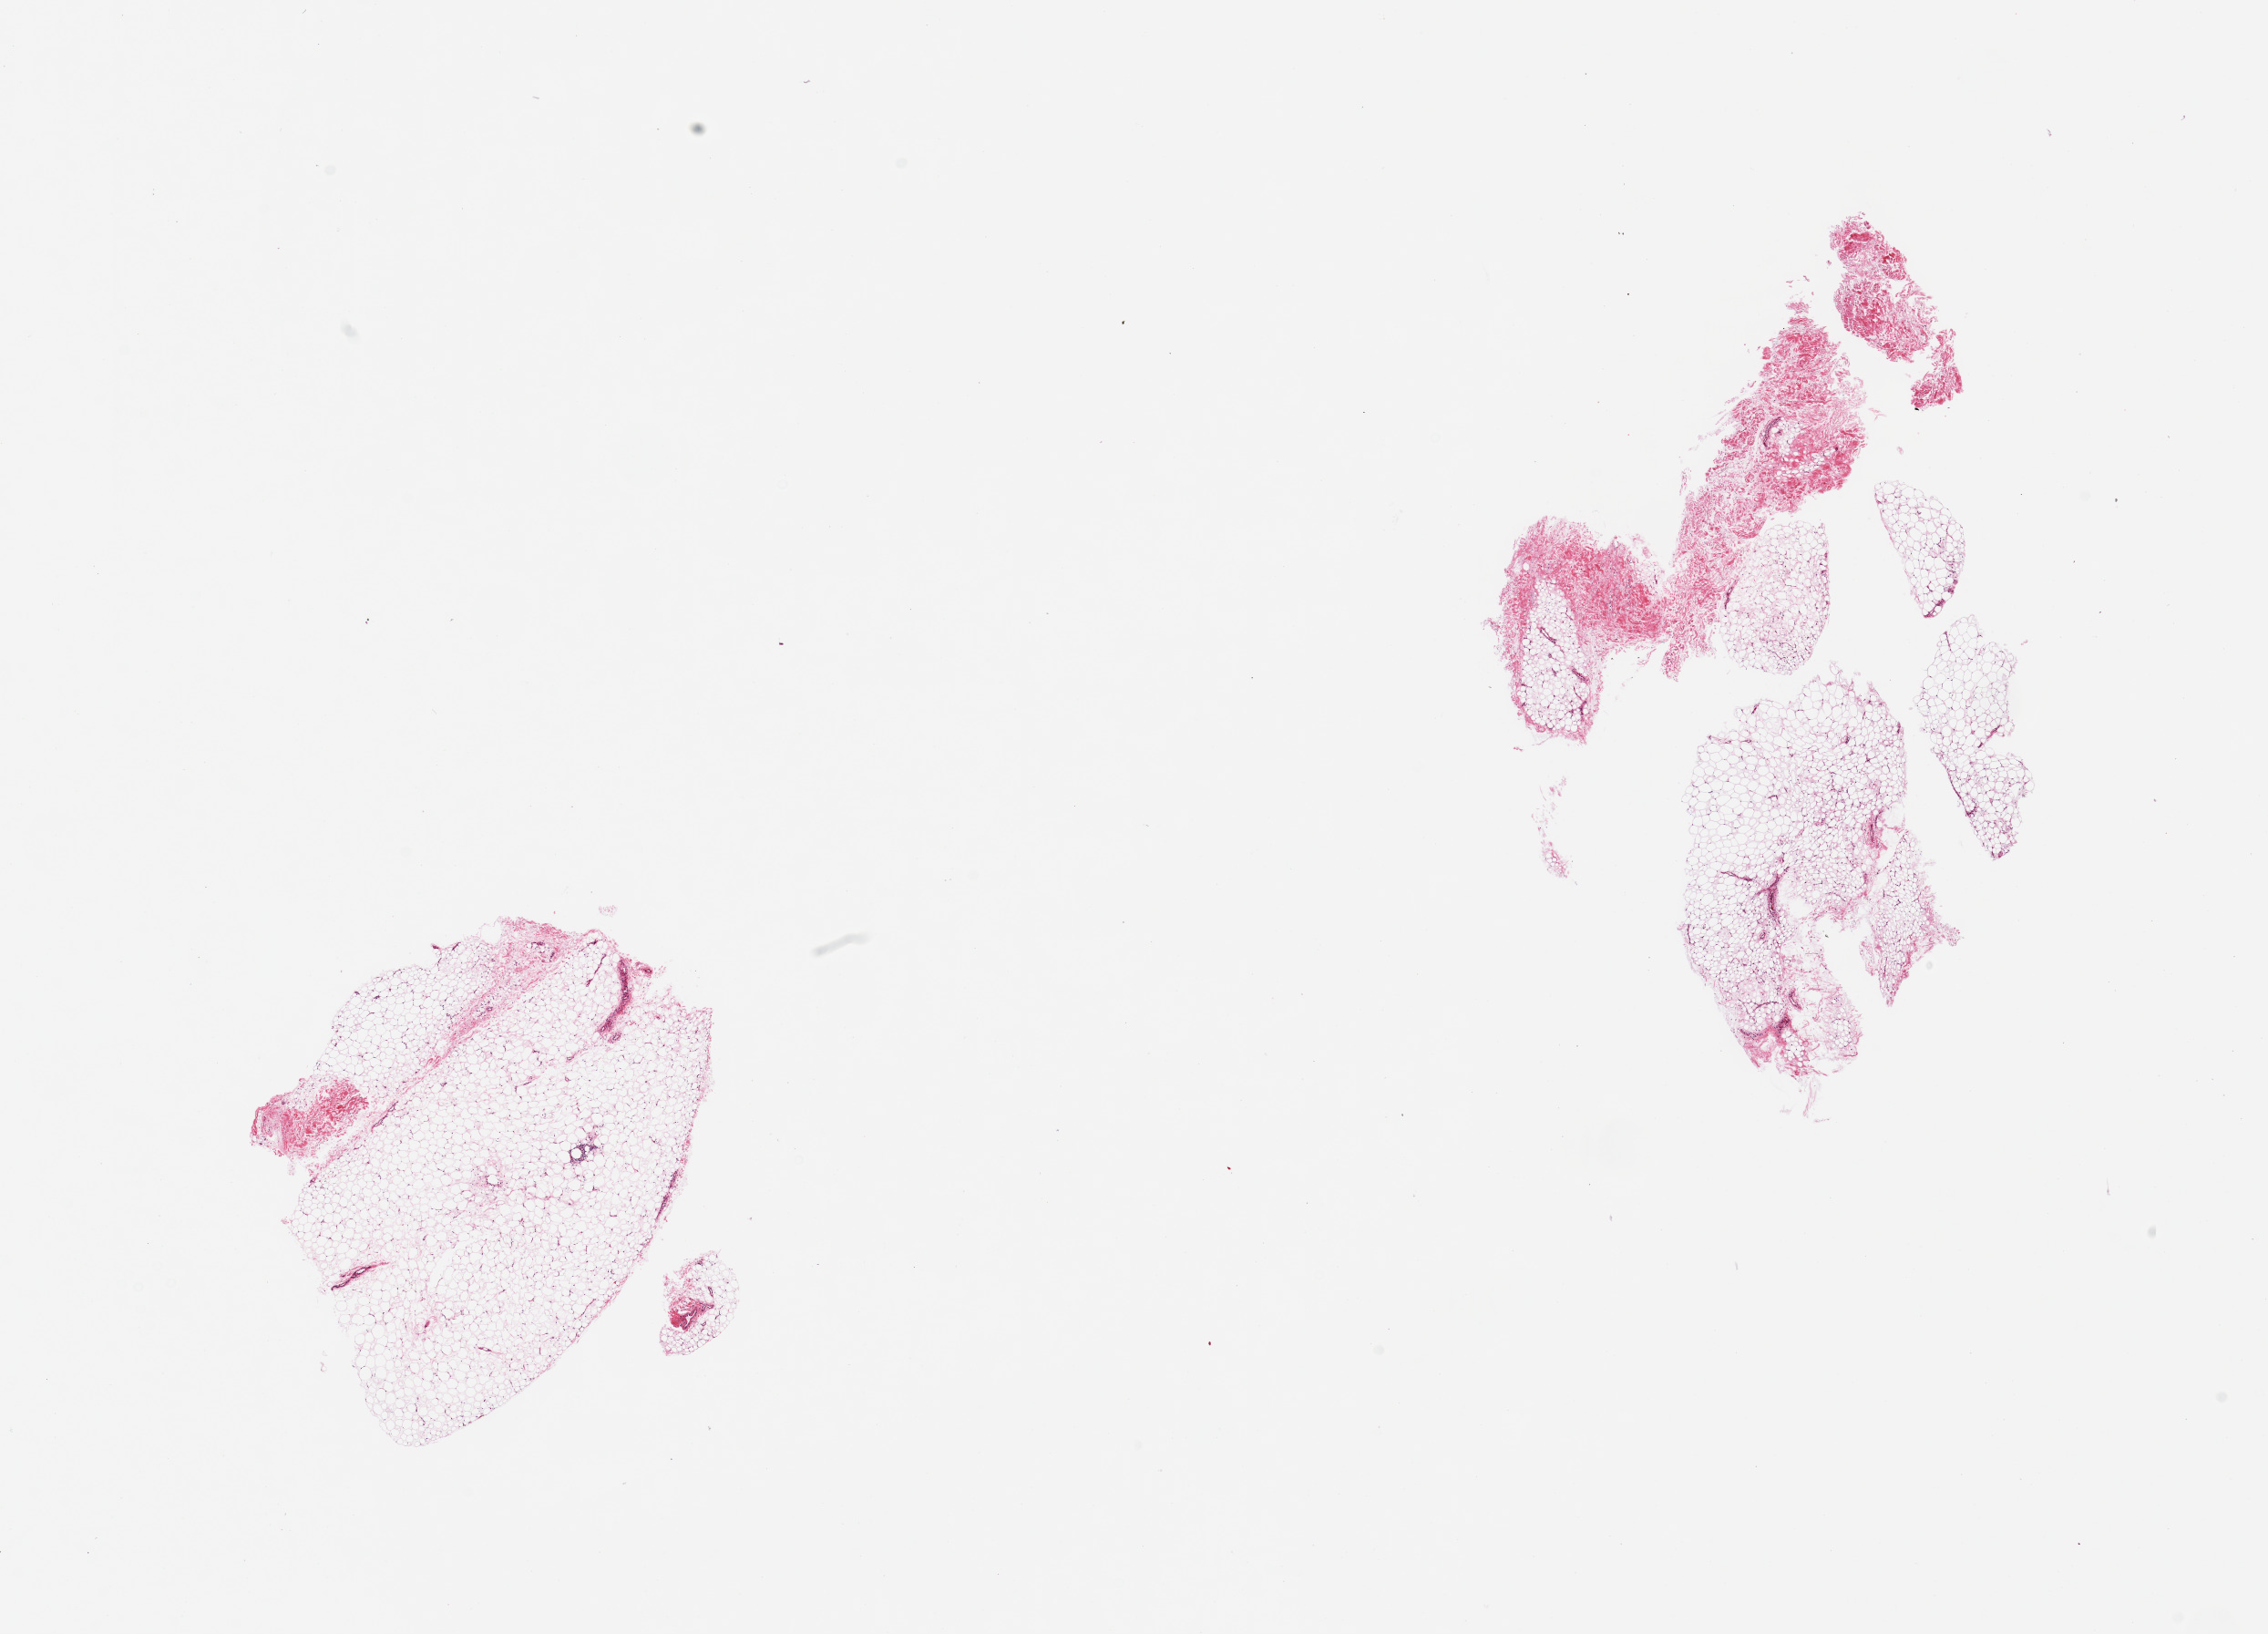
Digitized haematoxylin and eosin-stained section, brightfield — whole scanned area (about 19.7 x 14.2 mm) shown as a low-resolution overview, PAXgene-fixed paraffin-embedded (PFPE) section, sampled site (target tissue): adipose tissue, donor tissue sample. Donor sex: male.
Reviewer comment on this tissue sample: 2 pieces; 20% fibrous content in 1 piece, 5% in other.